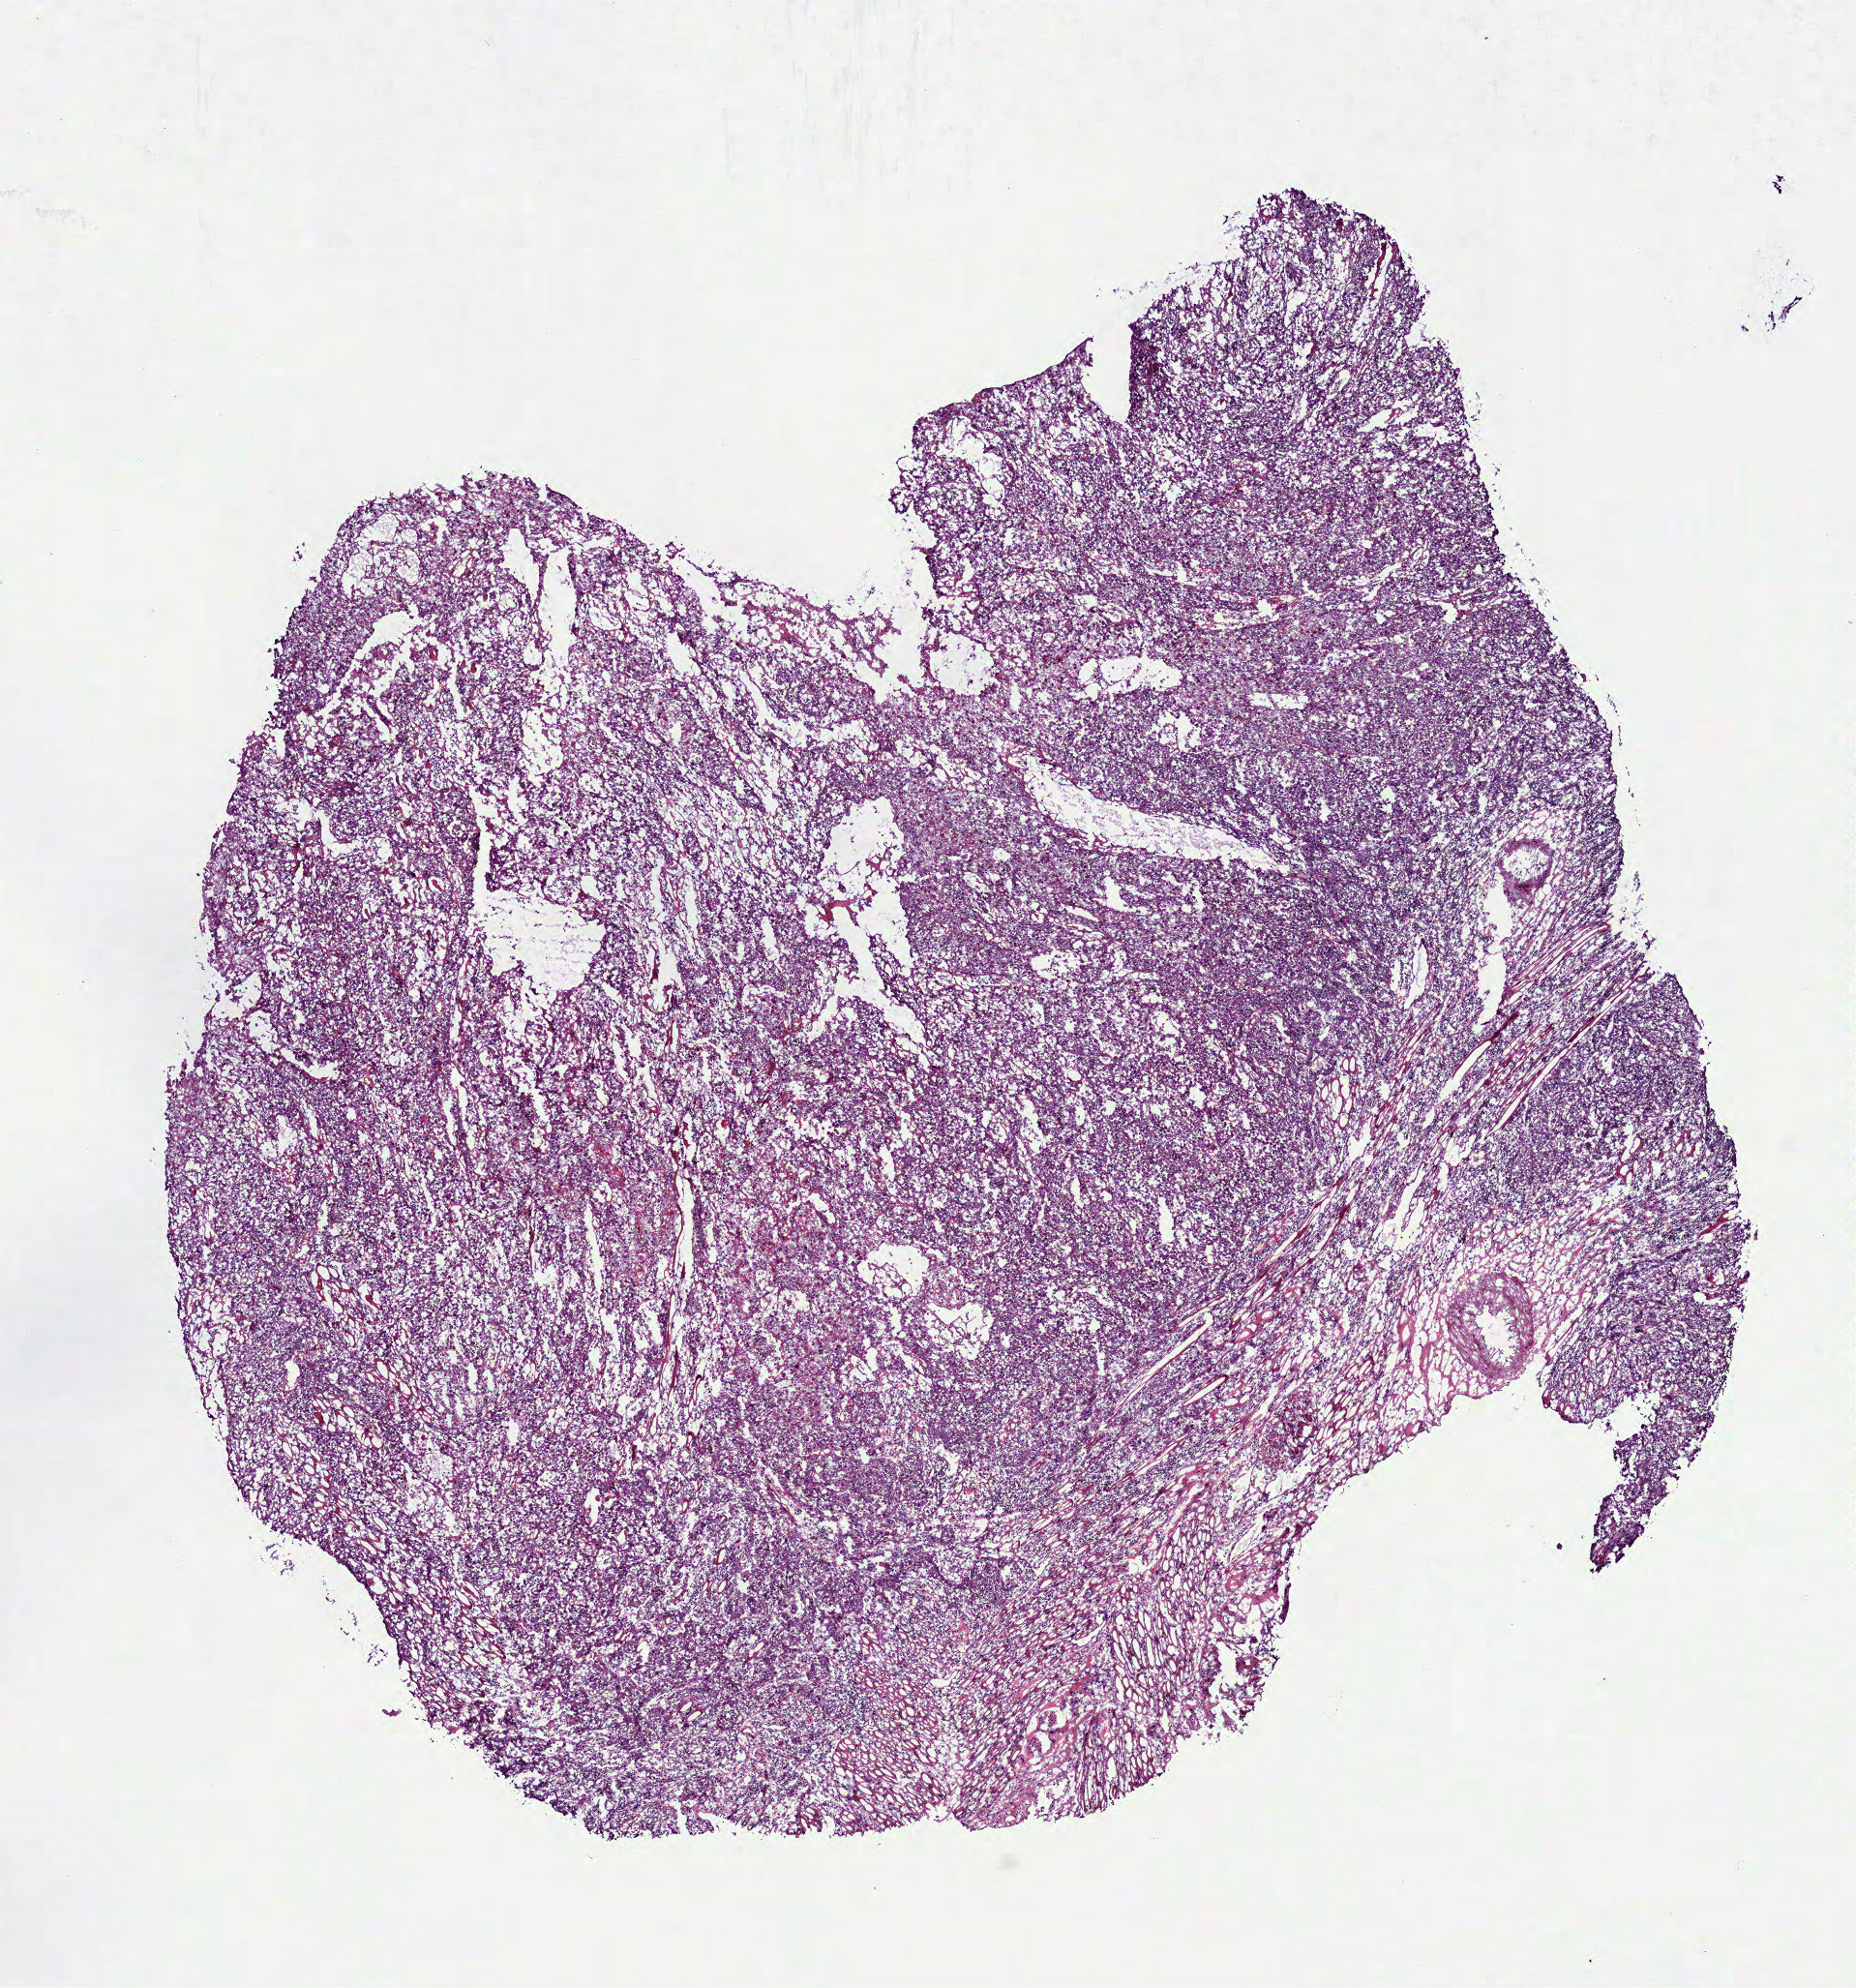
Whole-slide histology image, H&E-stained, low-resolution overview of the scanned area, about 7.7 x 8.3 mm (from a 40x scan), frozen section from the top of the tissue portion, head and neck, primary tumour sample. Male, age 55 years at initial diagnosis. Histologic grade: G2 (moderately differentiated). Pathologist review of this section (percent, as recorded): tumour cells 85%, tumour nuclei 80%, normal cells 0%, stromal cells 10%, necrosis 5%.
AJCC pathologic stage: IVA (7th edition). Pathologic diagnosis: Squamous cell carcinoma, NOS (tongue, NOS).